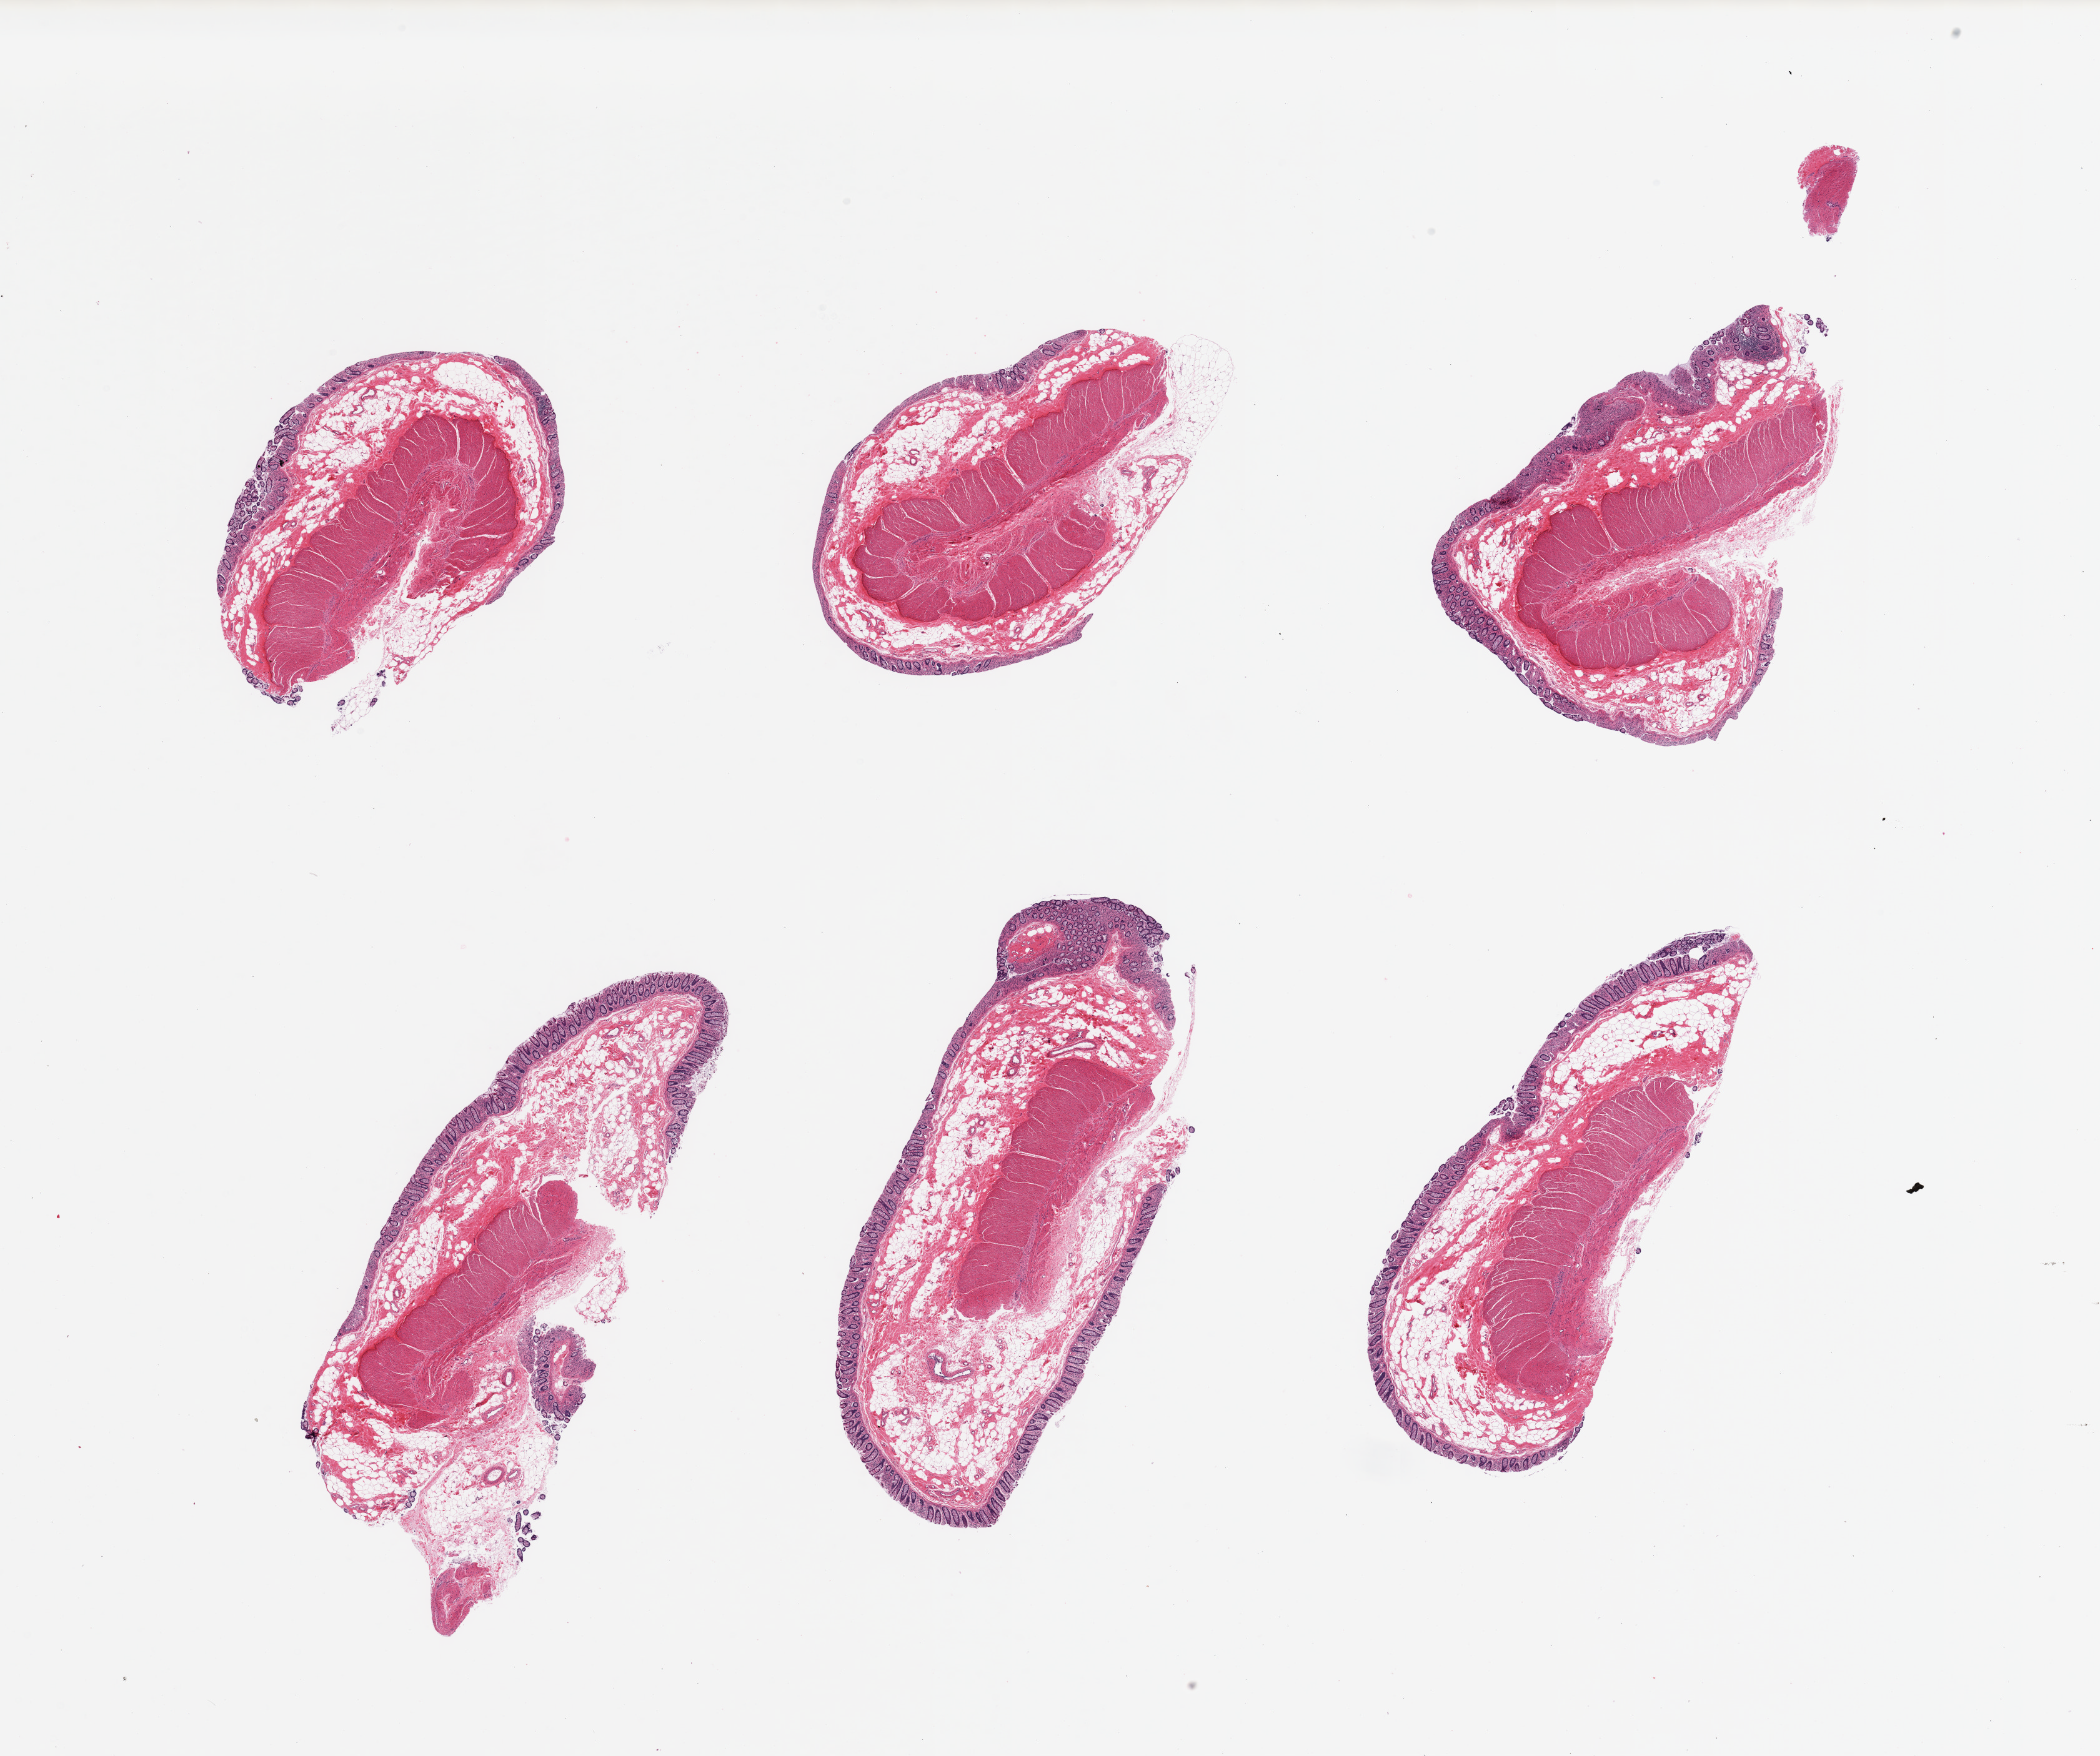
Digitized H&E-stained section, brightfield, a low-resolution overview of the entire scanned area, about 26.6 x 22.2 mm (from a 20x scan). PAXgene-fixed paraffin-embedded (PFPE) section. Section of transverse colon (target tissue). Tissue donor sample. Donor: male.
Reviewer comment on this tissue sample: 6 pieces, target mucosa ~0.3mm, moderate-severe advanced autolysis.